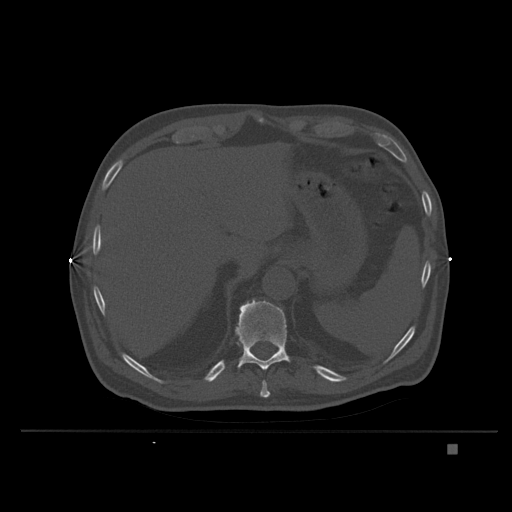
CT including the spine, one axial slice; slice 178 of 435 in the series (ordered by position); bone window (W 1800 / L 400 HU); 1.5 mm slice thickness; 512 × 512 image matrix, field of view 434 × 434 mm. Patient: male, 73 years. From the clinical record (not read from this slice): primary cancer: skin.
Structures marked on this image (semi-automatic segmentation, software-assisted and operator-edited):
- T10 vertebra: bounding box <260,380,271,398> (left, top, right, bottom; pixels)
- T11 vertebra: <235,298,291,370>